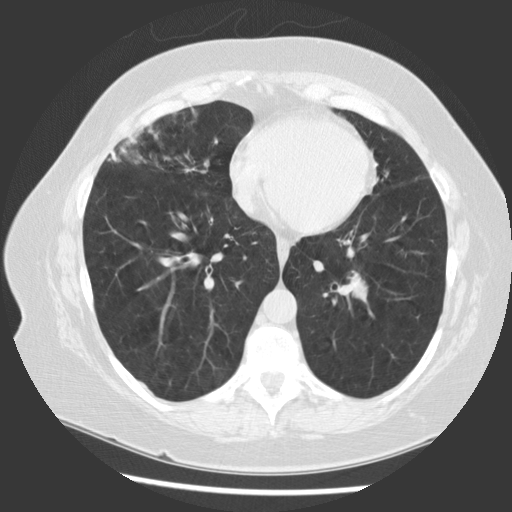
Low-dose screening chest CT, one axial slice; position 53 of 130 along the scan axis; reconstruction kernel STANDARD; 120 kVp; lung window (W 1500 / L -600 HU); 2.5 mm slice thickness; 512 × 512 image matrix, field of view 340 × 340 mm.
Outlined on this slice (expert manual segmentation):
- lesion 1 (tumor, hilum of left lung): bounding box [x1, y1, x2, y2] px = [348, 275, 367, 300]